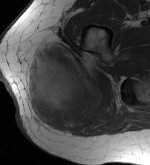
MRI of an extremity soft-tissue mass, one axial slice. Slice 21 of 56 in the series (ordered by position). MR volume resampled by the dataset authors to the PET/CT grid (not the native acquisition matrix). 3.27 mm slice thickness. 150 × 165 image matrix, field of view 146 × 161 mm. Female patient. From the clinical record (not read from this slice): histological type: epithelioid sarcoma with vascular differentiation; site of the primary tumour: right buttock.
Annotated regions visible in this slice (expert contour drawn on MRI and transferred to this co-registered scan by the dataset authors):
- gross tumour volume (mass): box from (x=25, y=42) to (x=111, y=134) px